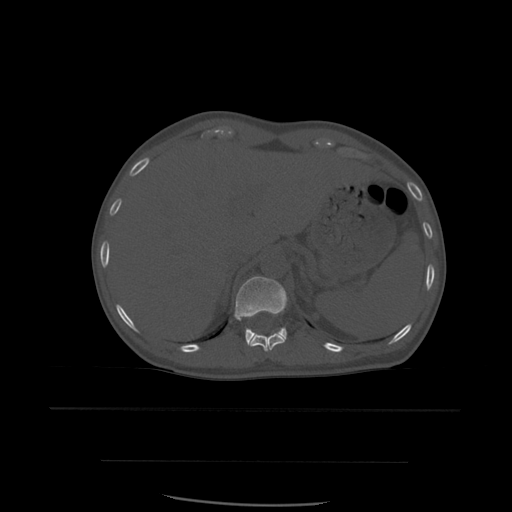
CT including the spine, one axial slice; slice 286 of 574 in the series (ordered by position); bone window (W 1800 / L 400 HU); 512 × 512 image matrix. Patient age 48 years. From the clinical record (not read from this slice): primary cancer: lung; vertebrae with lytic lesions (as recorded): T11.
Outlined on this slice (semi-automatically segmented with operator editing):
- T11 vertebra: bounding box <249,332,286,352> (left, top, right, bottom; pixels)
- T12 vertebra: <235,277,287,345>